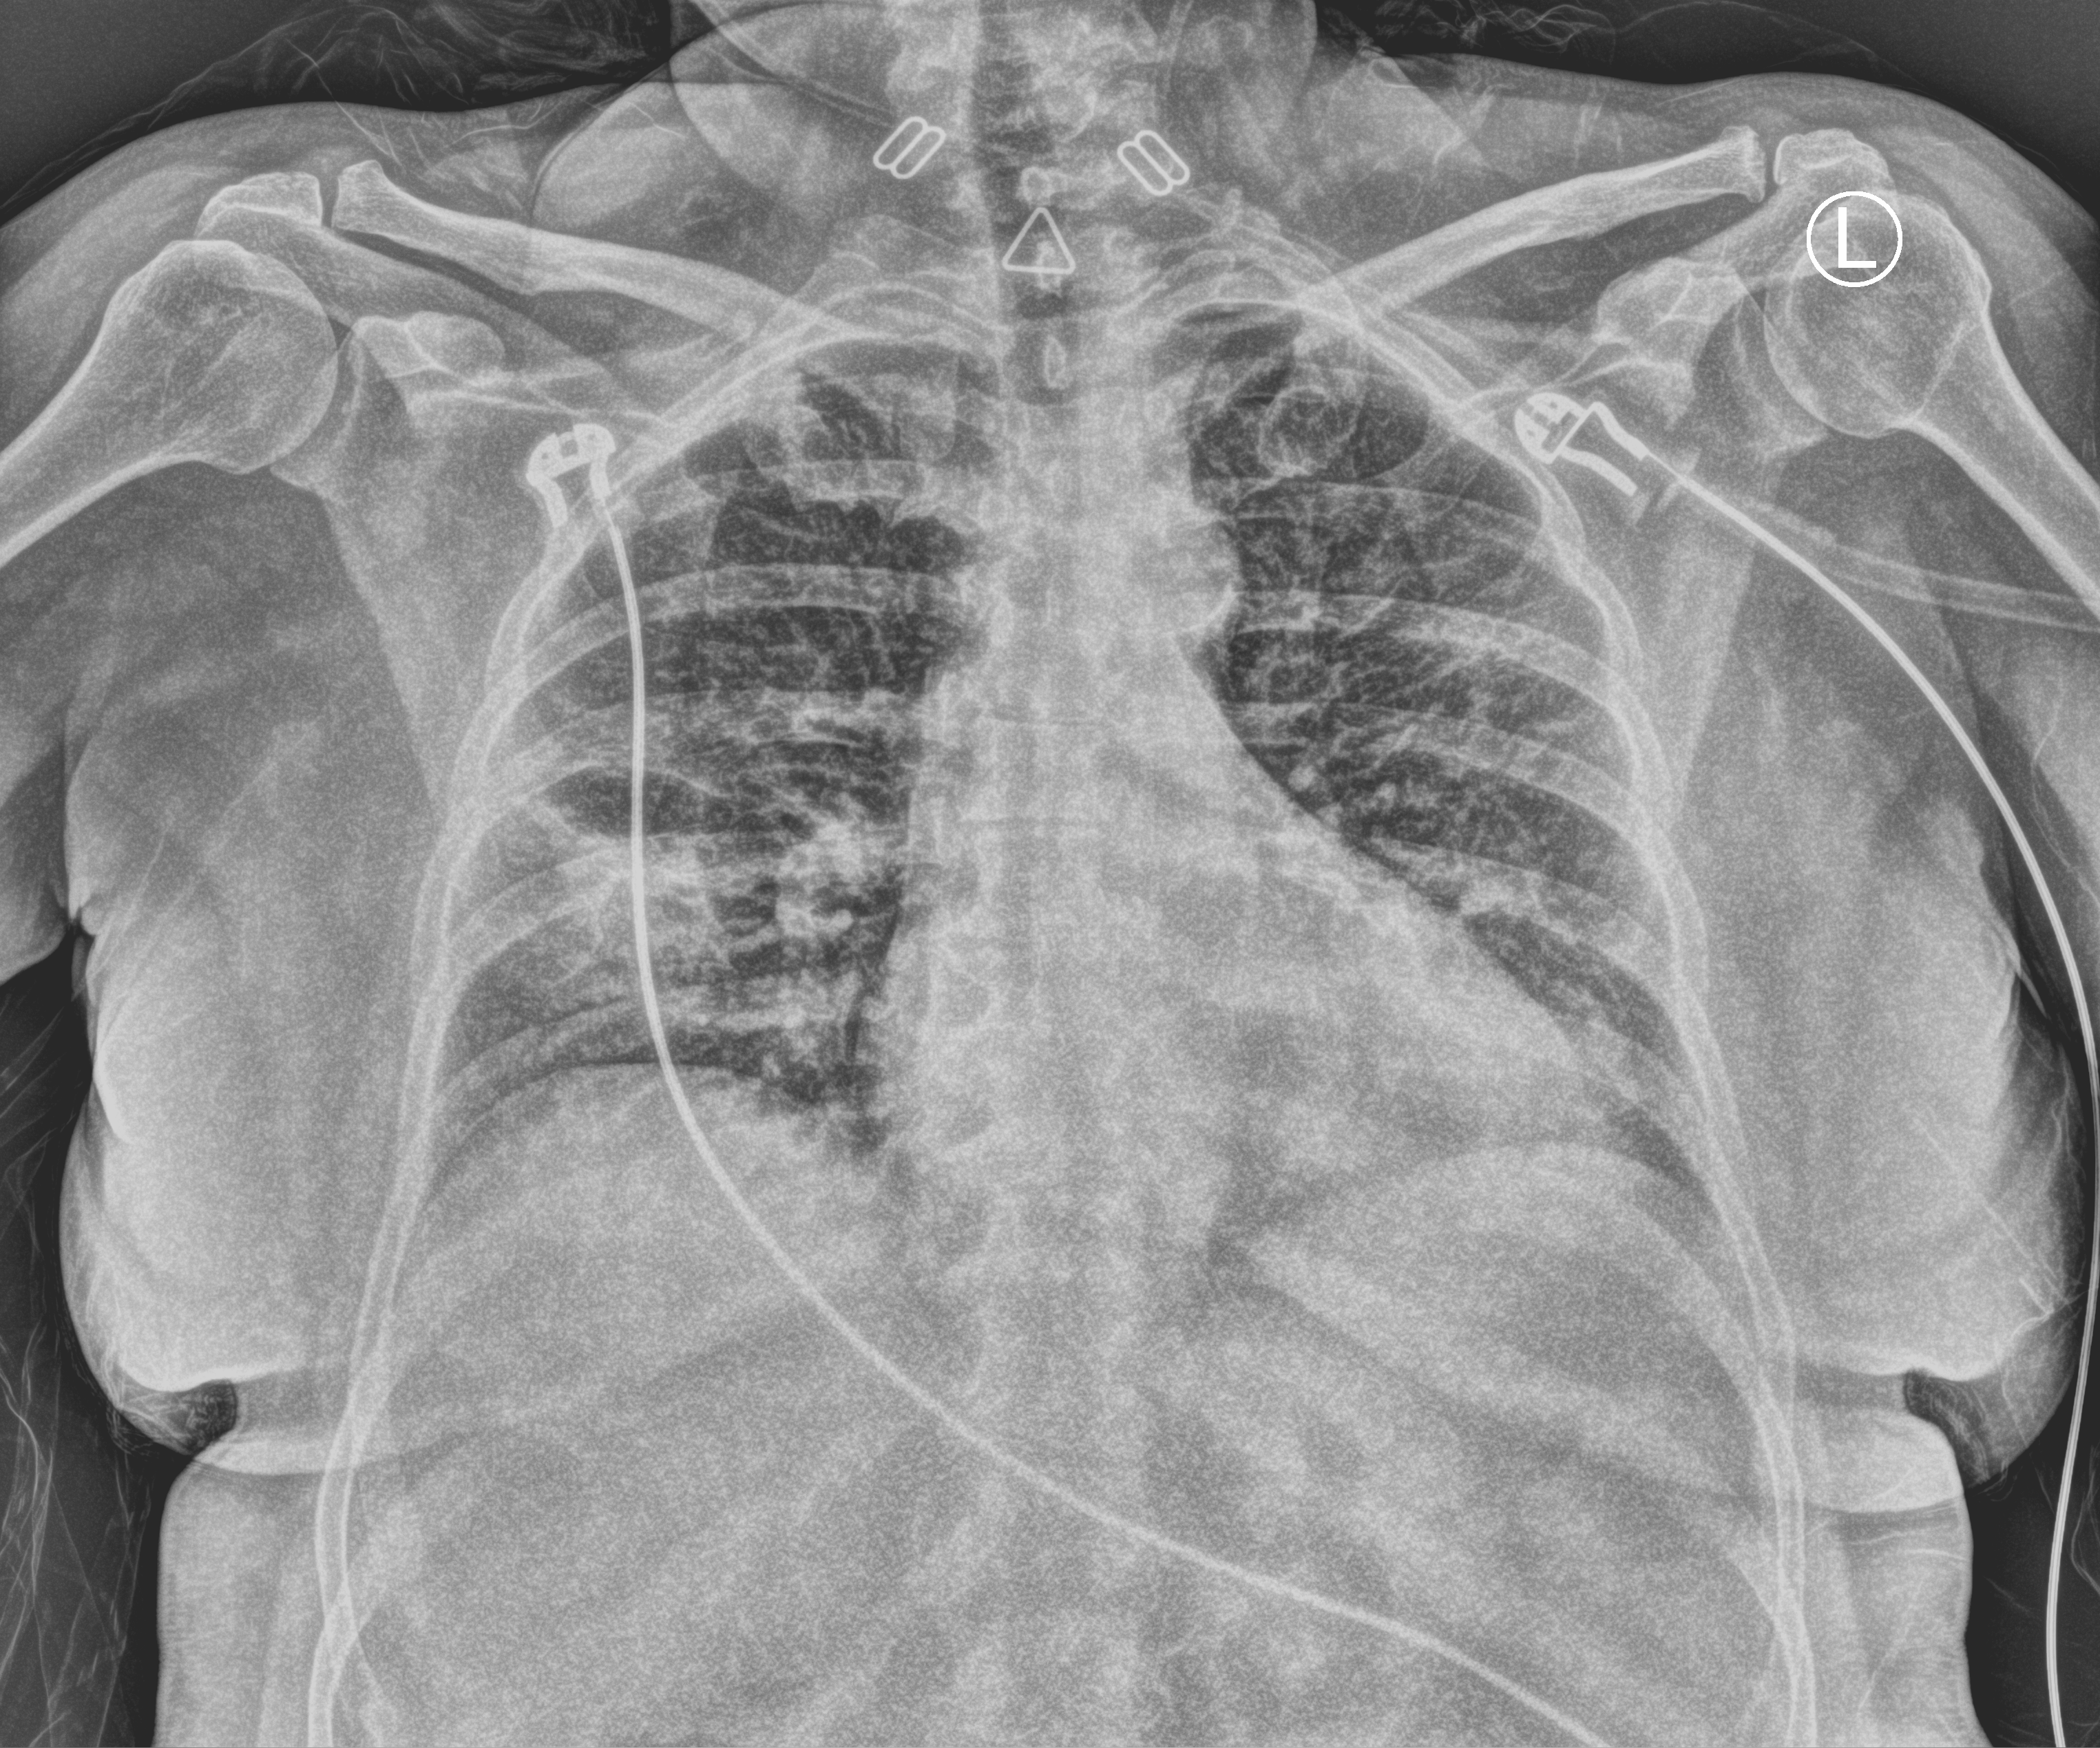
Portable chest radiograph; anteroposterior (AP) projection. Patient hospitalised with COVID-19; female, aged 60–74 years.
Admission-level facts for this patient (not findings on this image; timing relative to this image not recorded):
- chronic kidney disease (admission record): no
- admitted to intensive care during this hospital stay: yes